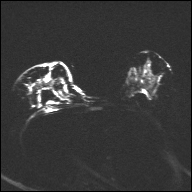
Breast MRI, one axial slice. Diffusion-weighted series; image 2 of 4 stored at this slice position (different b-values; order by instance number). 1.5 T. 192 × 192 image matrix, field of view 360 × 360 mm. Female patient.
Outlined on this slice (expert manual segmentation):
- tumour on diffusion-weighted imaging: bounding box (x1, y1, x2, y2) in pixels: (50, 80, 55, 86)